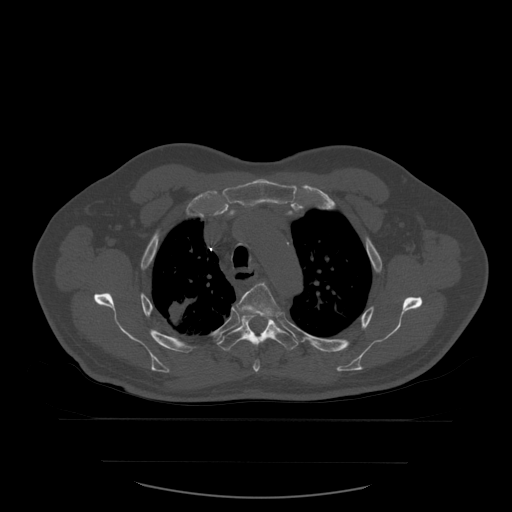
CT including the spine, one axial slice; slice 433 of 590 in the series (ordered by position); bone window (W 1800 / L 400 HU); 512 × 512 image matrix, field of view 479 × 479 mm. Patient age 71 years. From the clinical record (not read from this slice): primary cancer: lung.
Annotated regions visible in this slice (semi-automatically segmented with operator editing):
- T4 vertebra: box from (x=236, y=283) to (x=281, y=372) px
- T5 vertebra: (x=217, y=313)–(x=299, y=351)